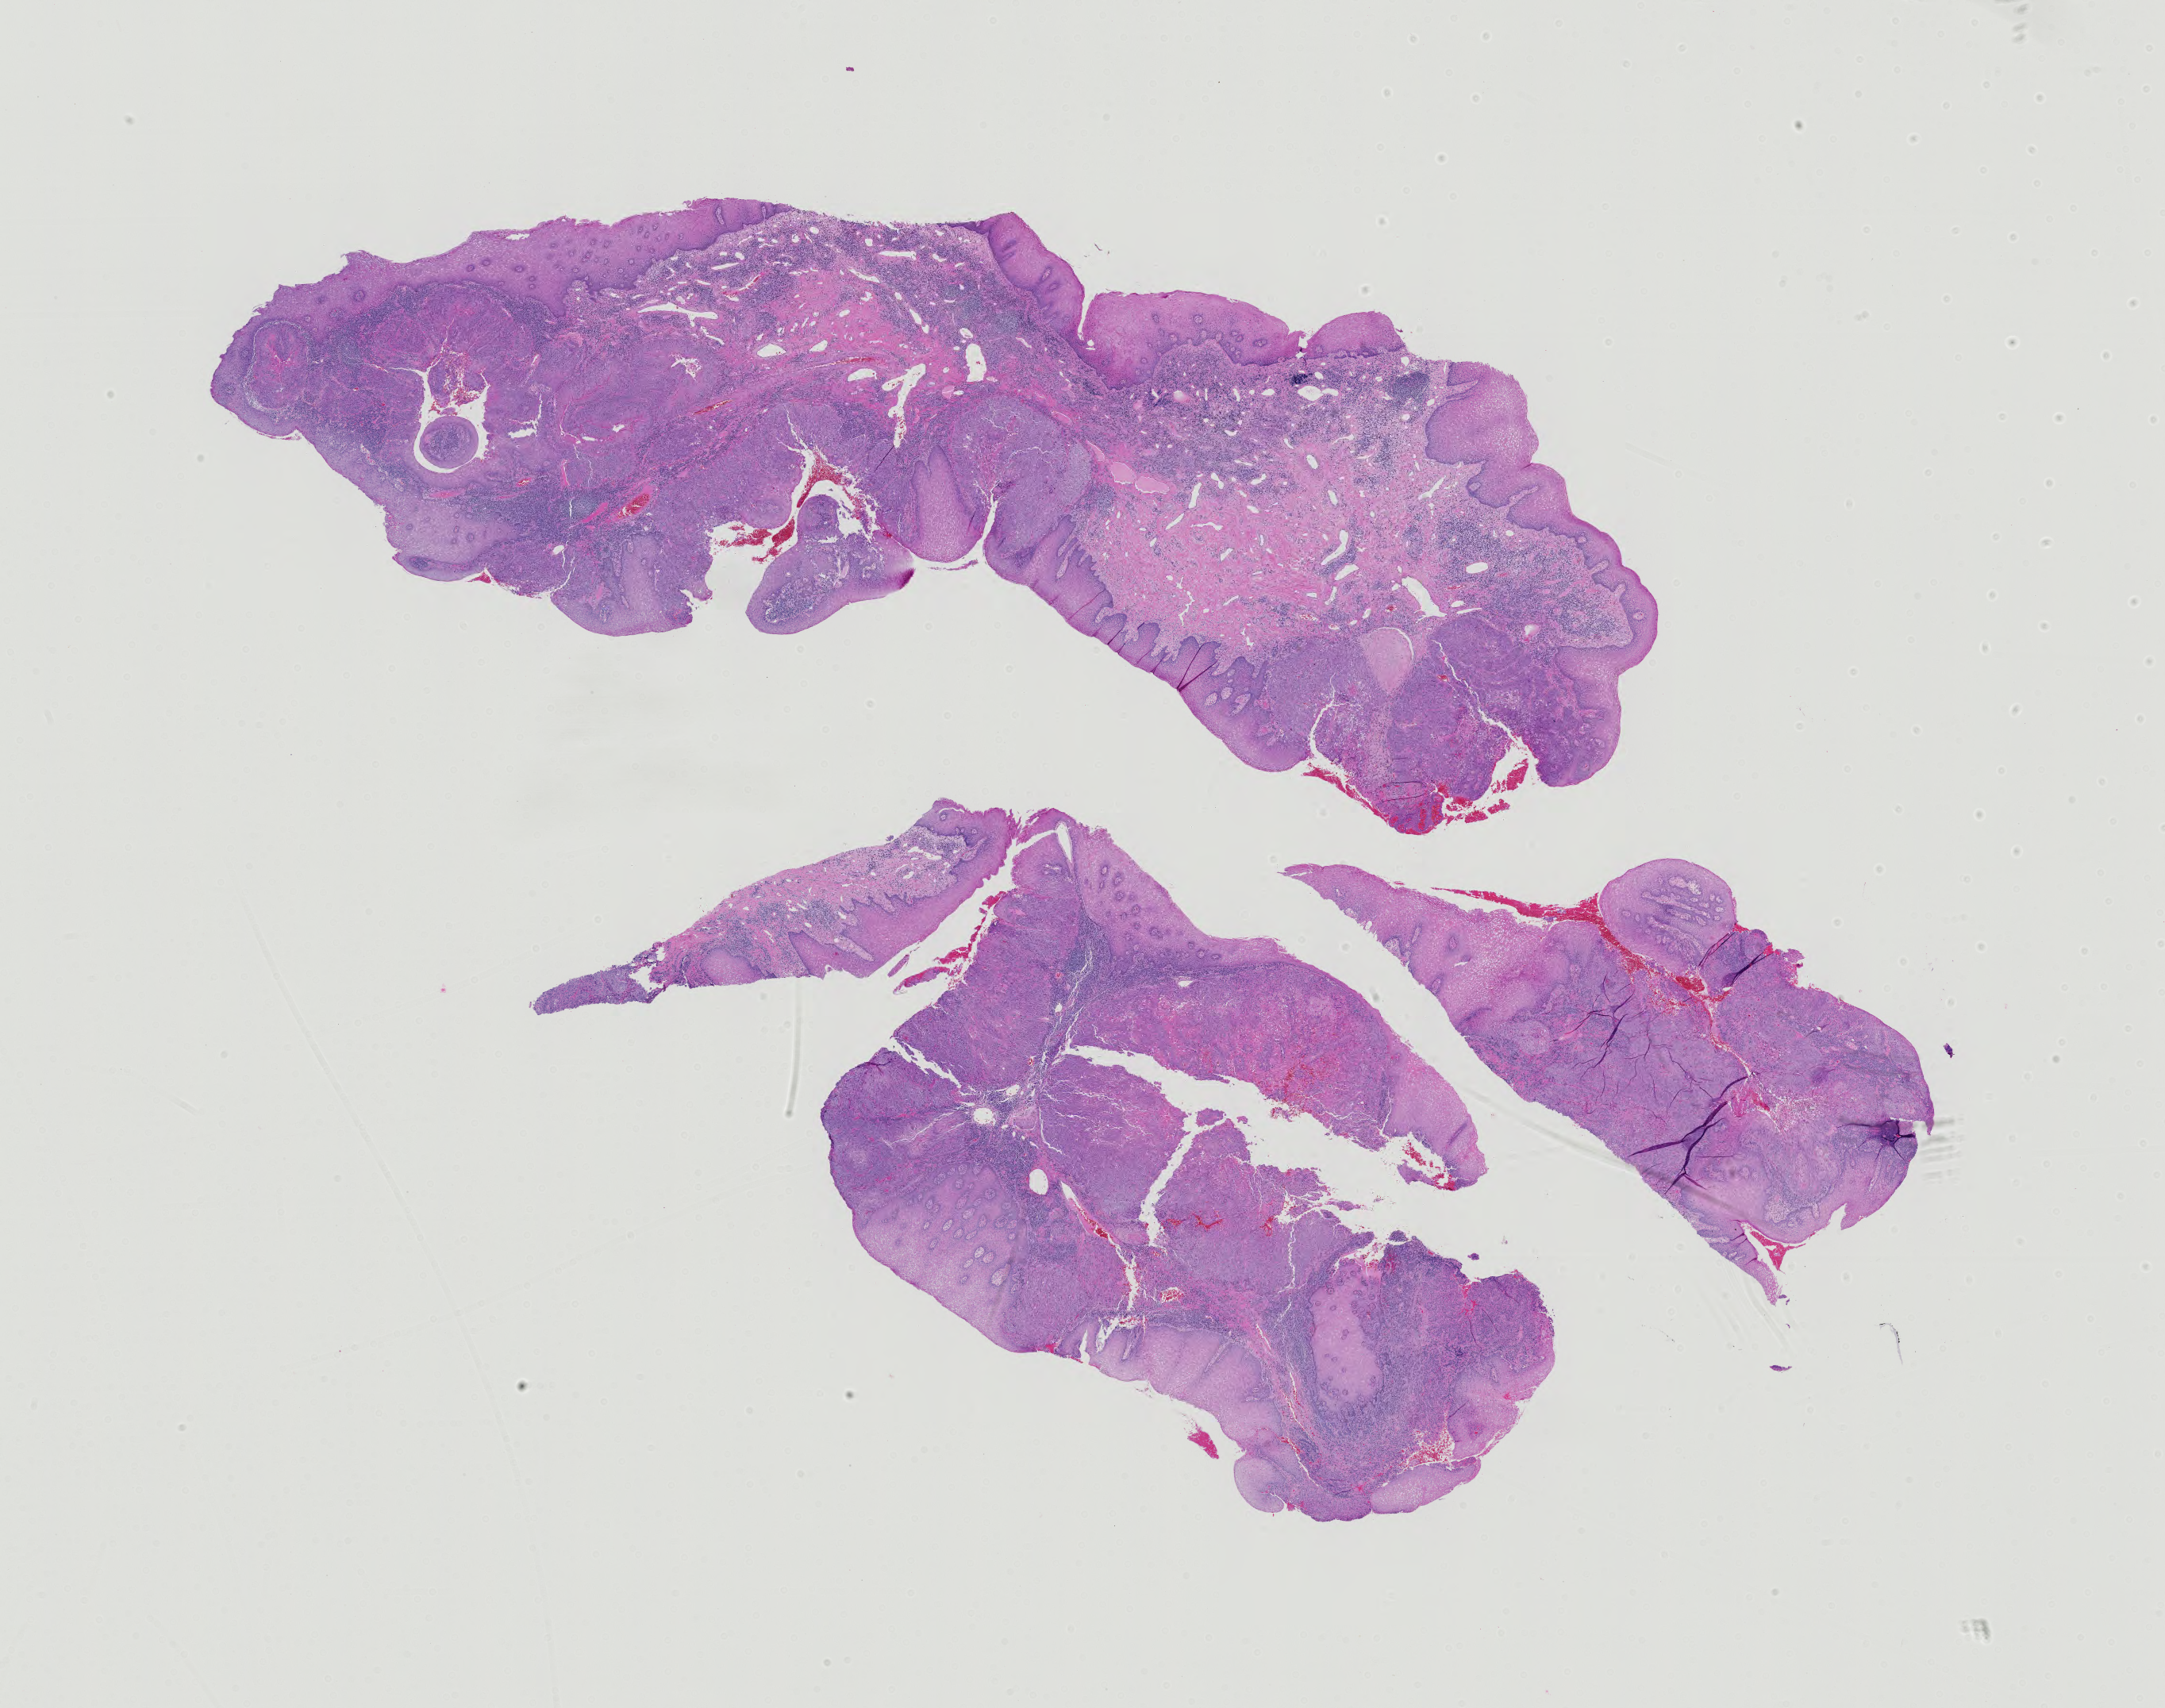
Hematoxylin and eosin (H&E) stained whole-slide image, whole scanned area (about 19.8 x 15.6 mm) shown as a low-resolution overview. Formalin-fixed paraffin-embedded (FFPE) diagnostic section. Sample: primary tumour, head and neck. Female patient; age at initial diagnosis 60 years. Histologic grade: G2 (moderately differentiated).
AJCC pathologic stage: IVC (7th edition). Pathologic diagnosis: Squamous cell carcinoma, NOS (larynx, NOS). Laterality: left.